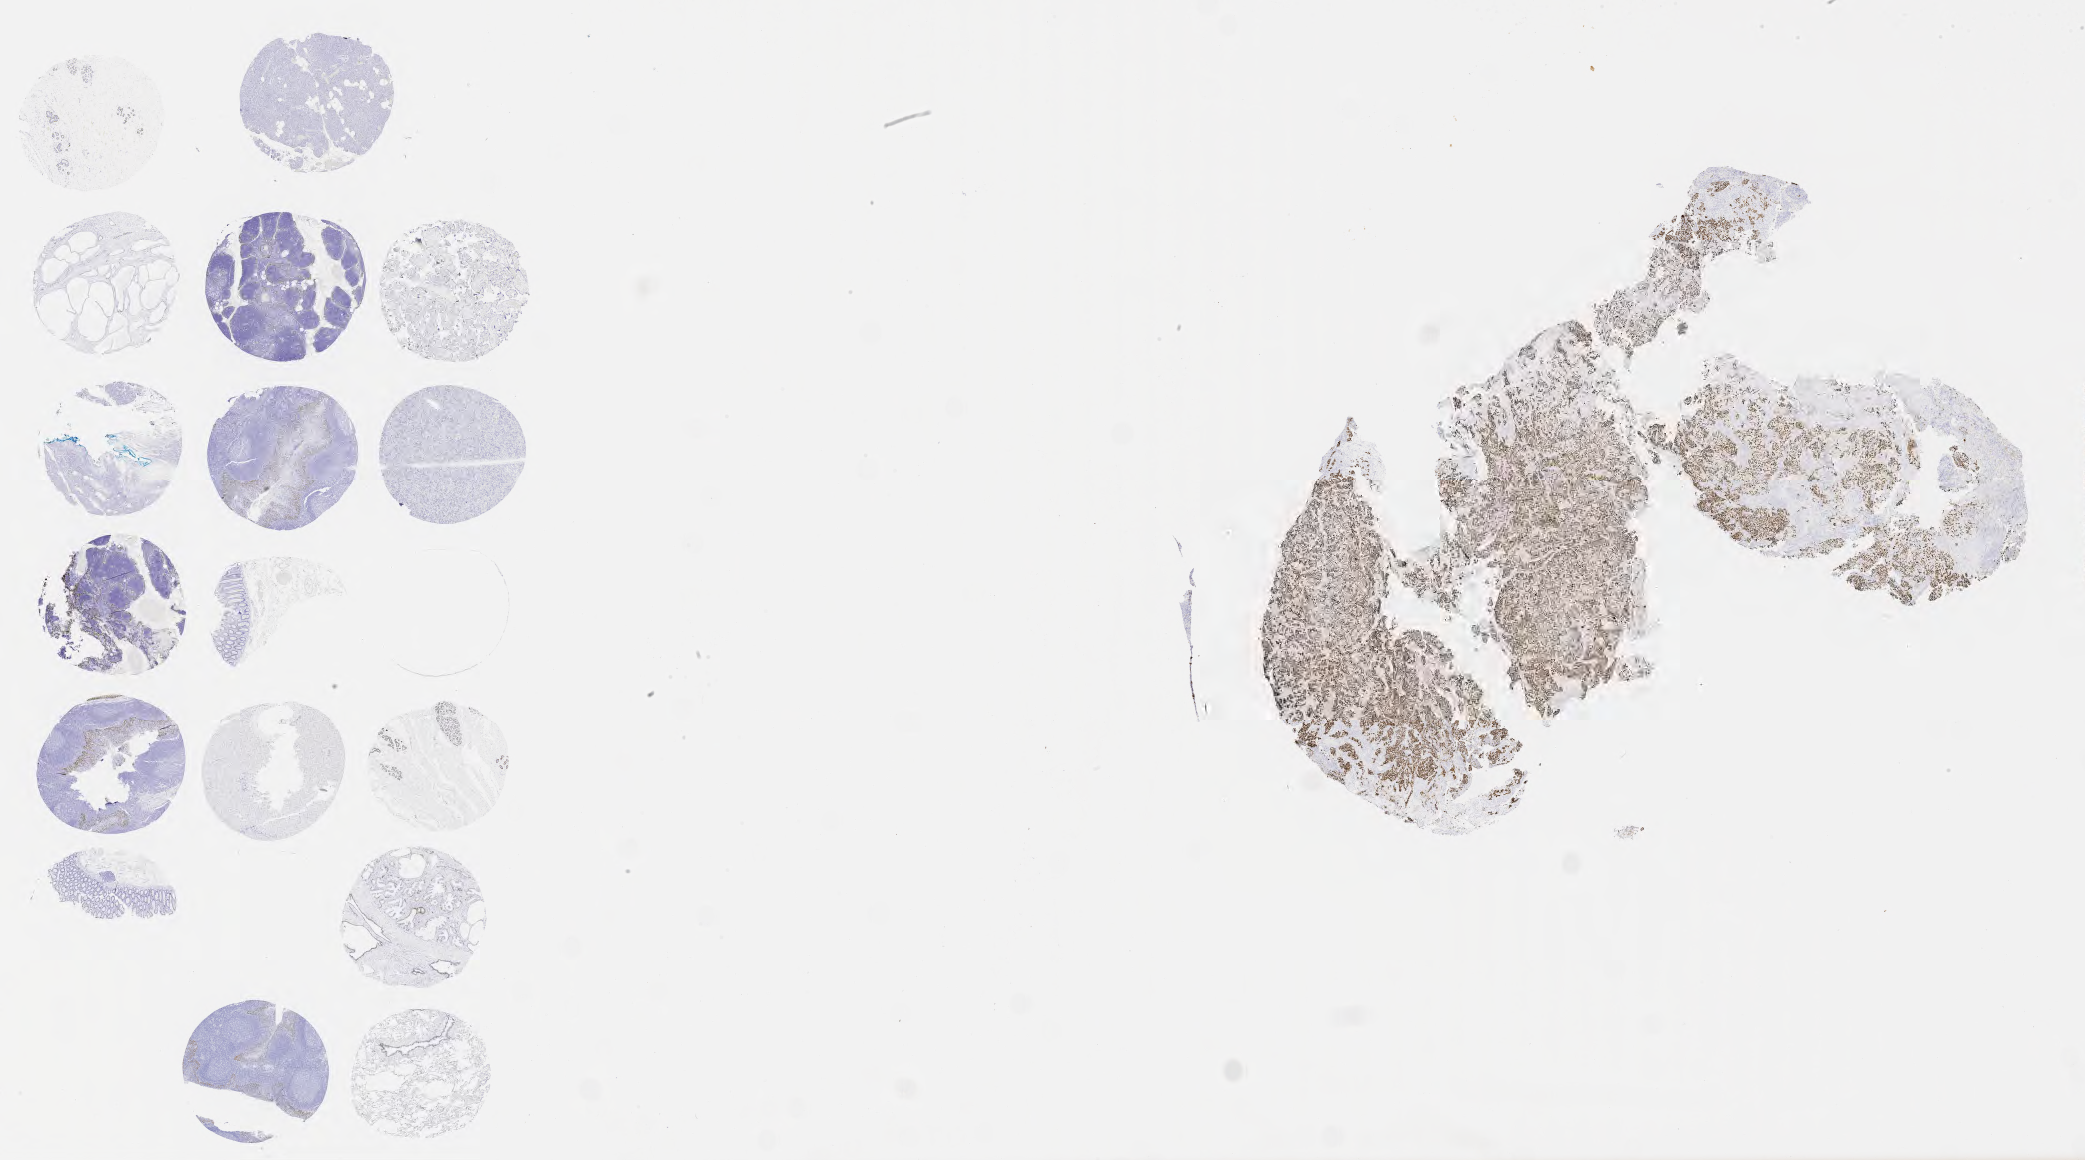
Immunohistochemistry (IHC) whole-slide image stained for p40, shown as a low-resolution overview of the whole scanned area (about 33.7 x 18.8 mm). Specimen: tumor tissue. Site: cervix. Patient female; 54 years old.
Histologic diagnosis: Adenocarcinoma, NOS.